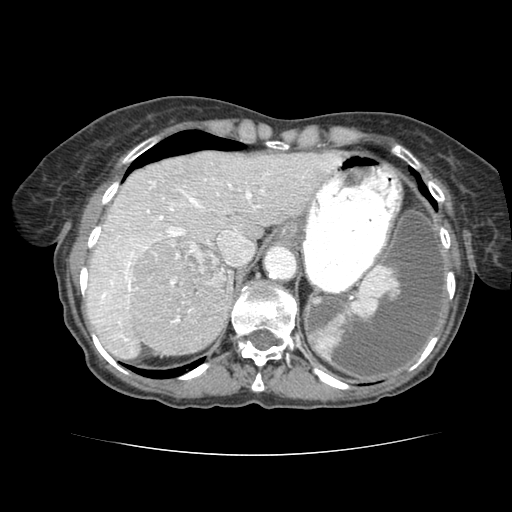
Contrast-enhanced abdominal CT (liver protocol), one axial slice; slice 60 of 77 in the series (ordered by position); reconstruction kernel STANDARD; soft-tissue window (W 400 / L 40 HU); 512 × 512 image matrix, field of view 340 × 340 mm. Case-level facts recorded for this patient, not image findings: diagnosis: hepatocellular carcinoma (patient treated with transarterial chemoembolisation; whether this scan precedes or follows treatment is not stated here); TNM stage (as recorded): Stage-I; Child-Pugh class: A; tumour differentiation: well differentiated; tumour nodularity: uninodular.
Outlined on this slice (semi-automatic segmentation, software-assisted and operator-edited):
- liver parenchyma outside the tumour (the mass and vessels are separate outlines, so this box may not span the whole liver): bounding box (x1, y1, x2, y2) in pixels: (80, 150, 334, 354)
- mass: (127, 237, 229, 349)
- liver vessels: (92, 175, 264, 334)